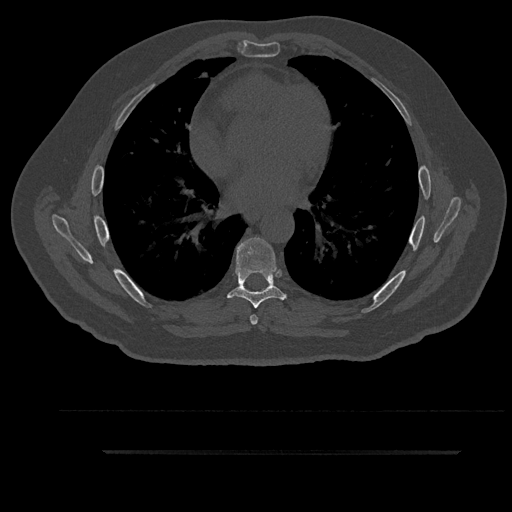
CT including the spine, one axial slice. Slice 532 of 797 in the series (ordered by position). Reconstruction kernel Br40s/3. Bone window (W 1800 / L 400 HU). 0.5 mm slice thickness. 512 × 512 image matrix, field of view 432 × 432 mm. Male patient, age 63 years. From the clinical record (not read from this slice): primary cancer: renal; vertebrae with lytic lesions (as recorded): T8.
Annotated regions visible in this slice (semi-automatic segmentation, software-assisted and operator-edited):
- T6 vertebra: box from (x=250, y=291) to (x=263, y=325) px
- T7 vertebra: (x=226, y=237)–(x=286, y=308)